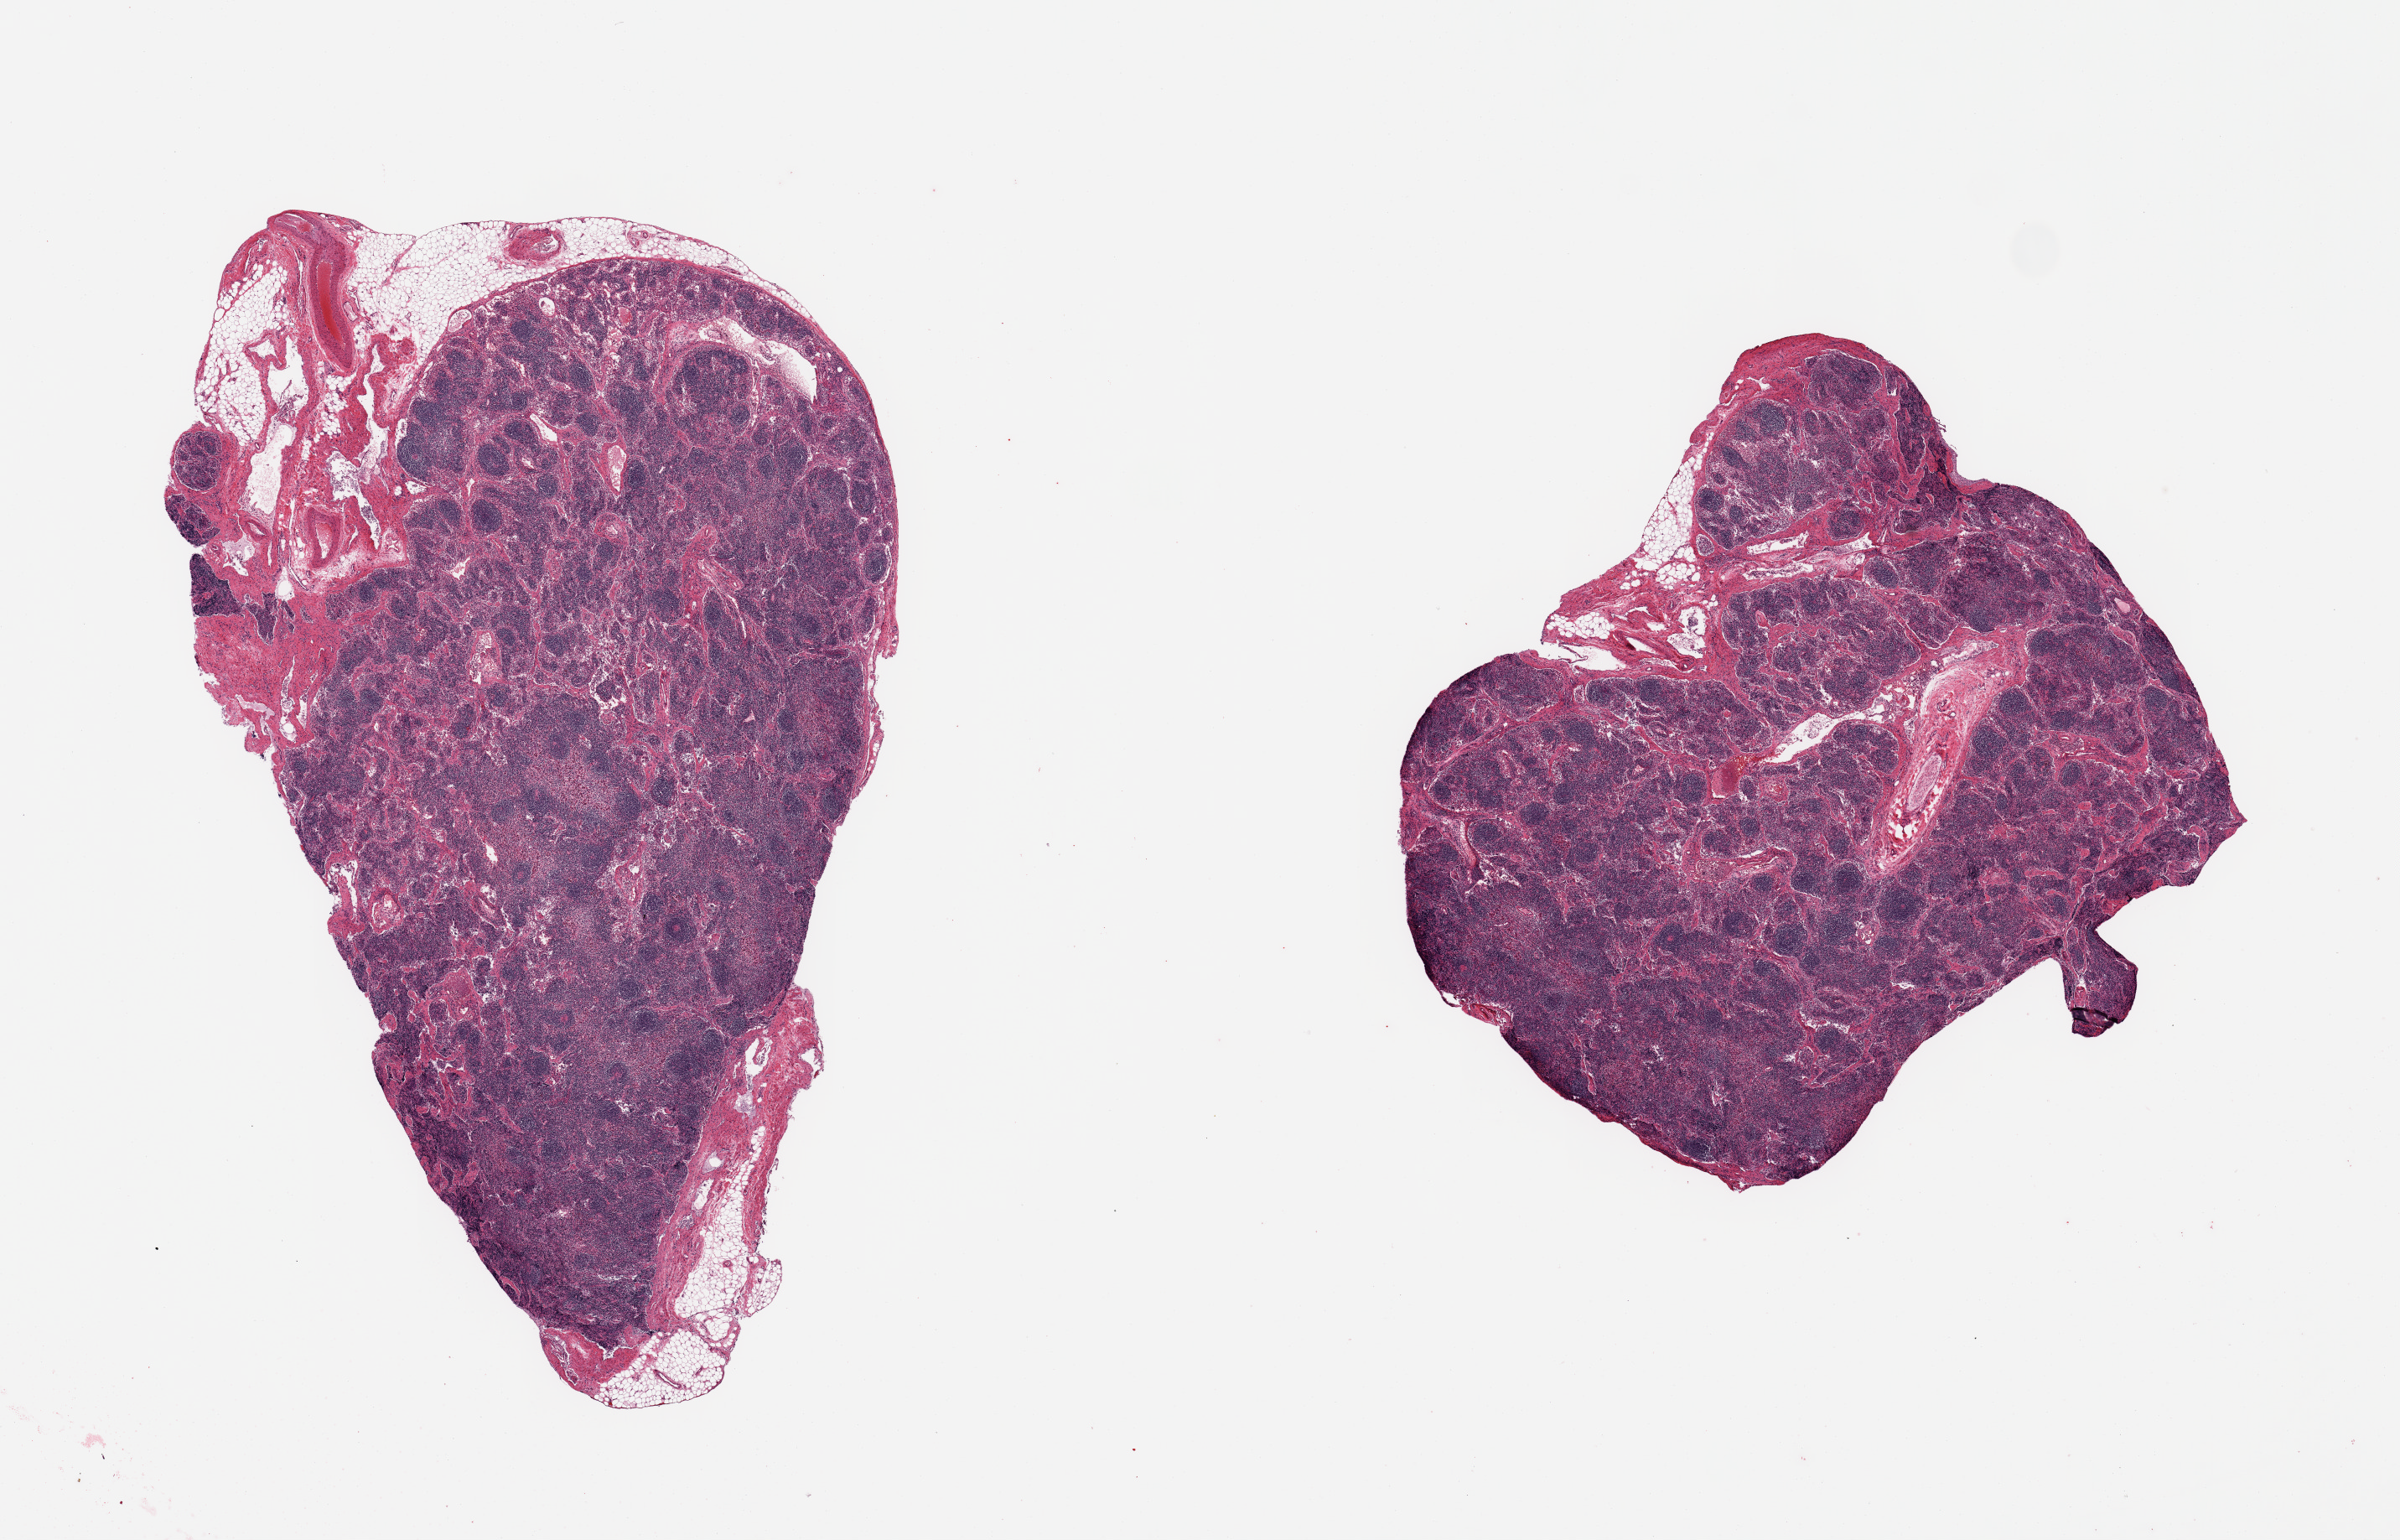
Whole-slide image, haematoxylin and eosin stain, brightfield — shown as a low-resolution overview of the whole scanned area (about 22.6 x 14.5 mm, slide scanned at 20x); PAXgene-fixed paraffin-embedded (PFPE) section; sampled site (target tissue): thyroid; tissue donor sample. Donor sex: male.
• review note (as recorded): 2 pieces; 2 lymph nodes, no thyroid